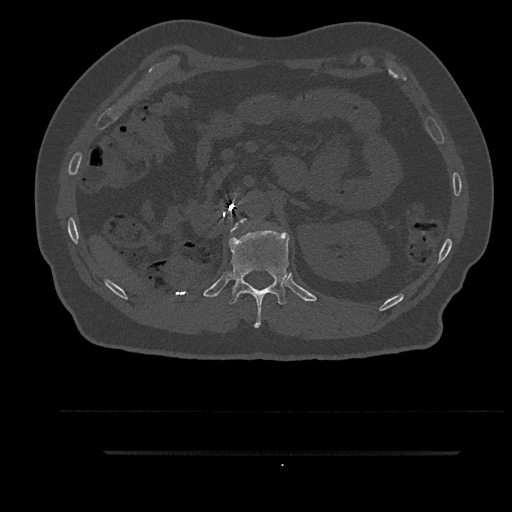
CT including the spine, one axial slice; position 234 of 797 along the scan axis; reconstruction kernel Br40s/3; 120 kVp; bone window (W 1800 / L 400 HU); 0.5 mm slice thickness; 512 × 512 image matrix, field of view 432 × 432 mm. Patient: male, 63 years. Case-level facts recorded for this patient, not image findings: primary cancer: renal; vertebrae with lytic lesions (as recorded): T8.
Structures marked on this image (semi-automatically segmented with operator editing):
- L1 vertebra: bounding box [x1, y1, x2, y2] px = [230, 220, 246, 232]
- T12 vertebra: [229, 230, 289, 328]